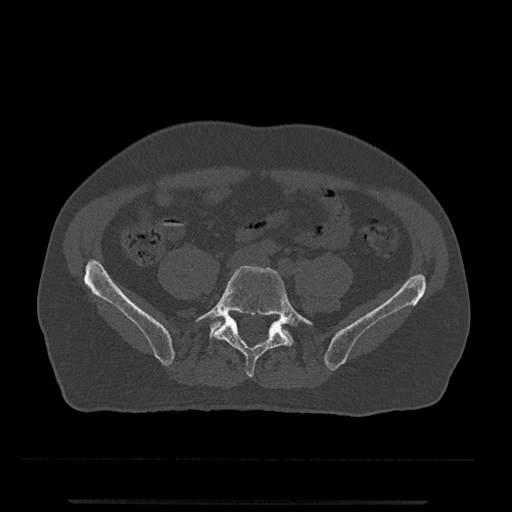
CT including the spine, one axial slice; position 70 of 797 along the scan axis; 120 kVp; bone window (W 1800 / L 400 HU); 0.5 mm slice thickness; 512 × 512 image matrix, field of view 419 × 419 mm. Patient: male, 63 years. Case-level facts recorded for this patient, not image findings: primary cancer: prostate.
Outlined on this slice (semi-automatically segmented with operator editing):
- L5 vertebra: bounding box [x1, y1, x2, y2] px = [192, 266, 315, 377]